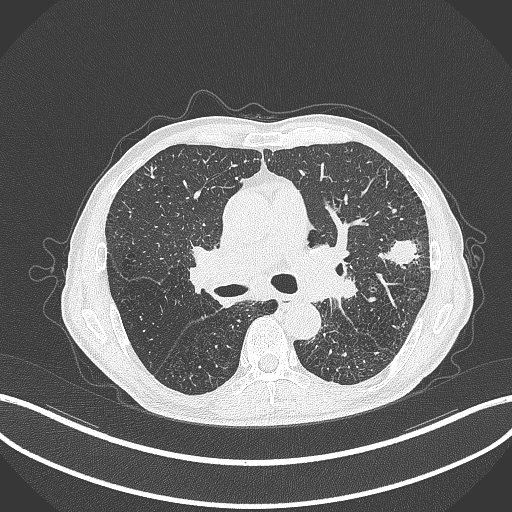
Chest CT, one axial slice. Slice 252 of 463 in the series (ordered by position). Reconstruction kernel B70f. 120 kVp. Lung window (W 1500 / L -600 HU). 1 mm slice thickness. 512 × 512 image matrix. Male patient, age 74 years. From the clinical record (not read from this slice): clinical TNM (as recorded): T2a N1 M0.
Outlined on this slice (bounding box drawn by a radiologist):
- lung tumour (recorded histology: adenocarcinoma): bounding box <376,238,423,271> (left, top, right, bottom; pixels)